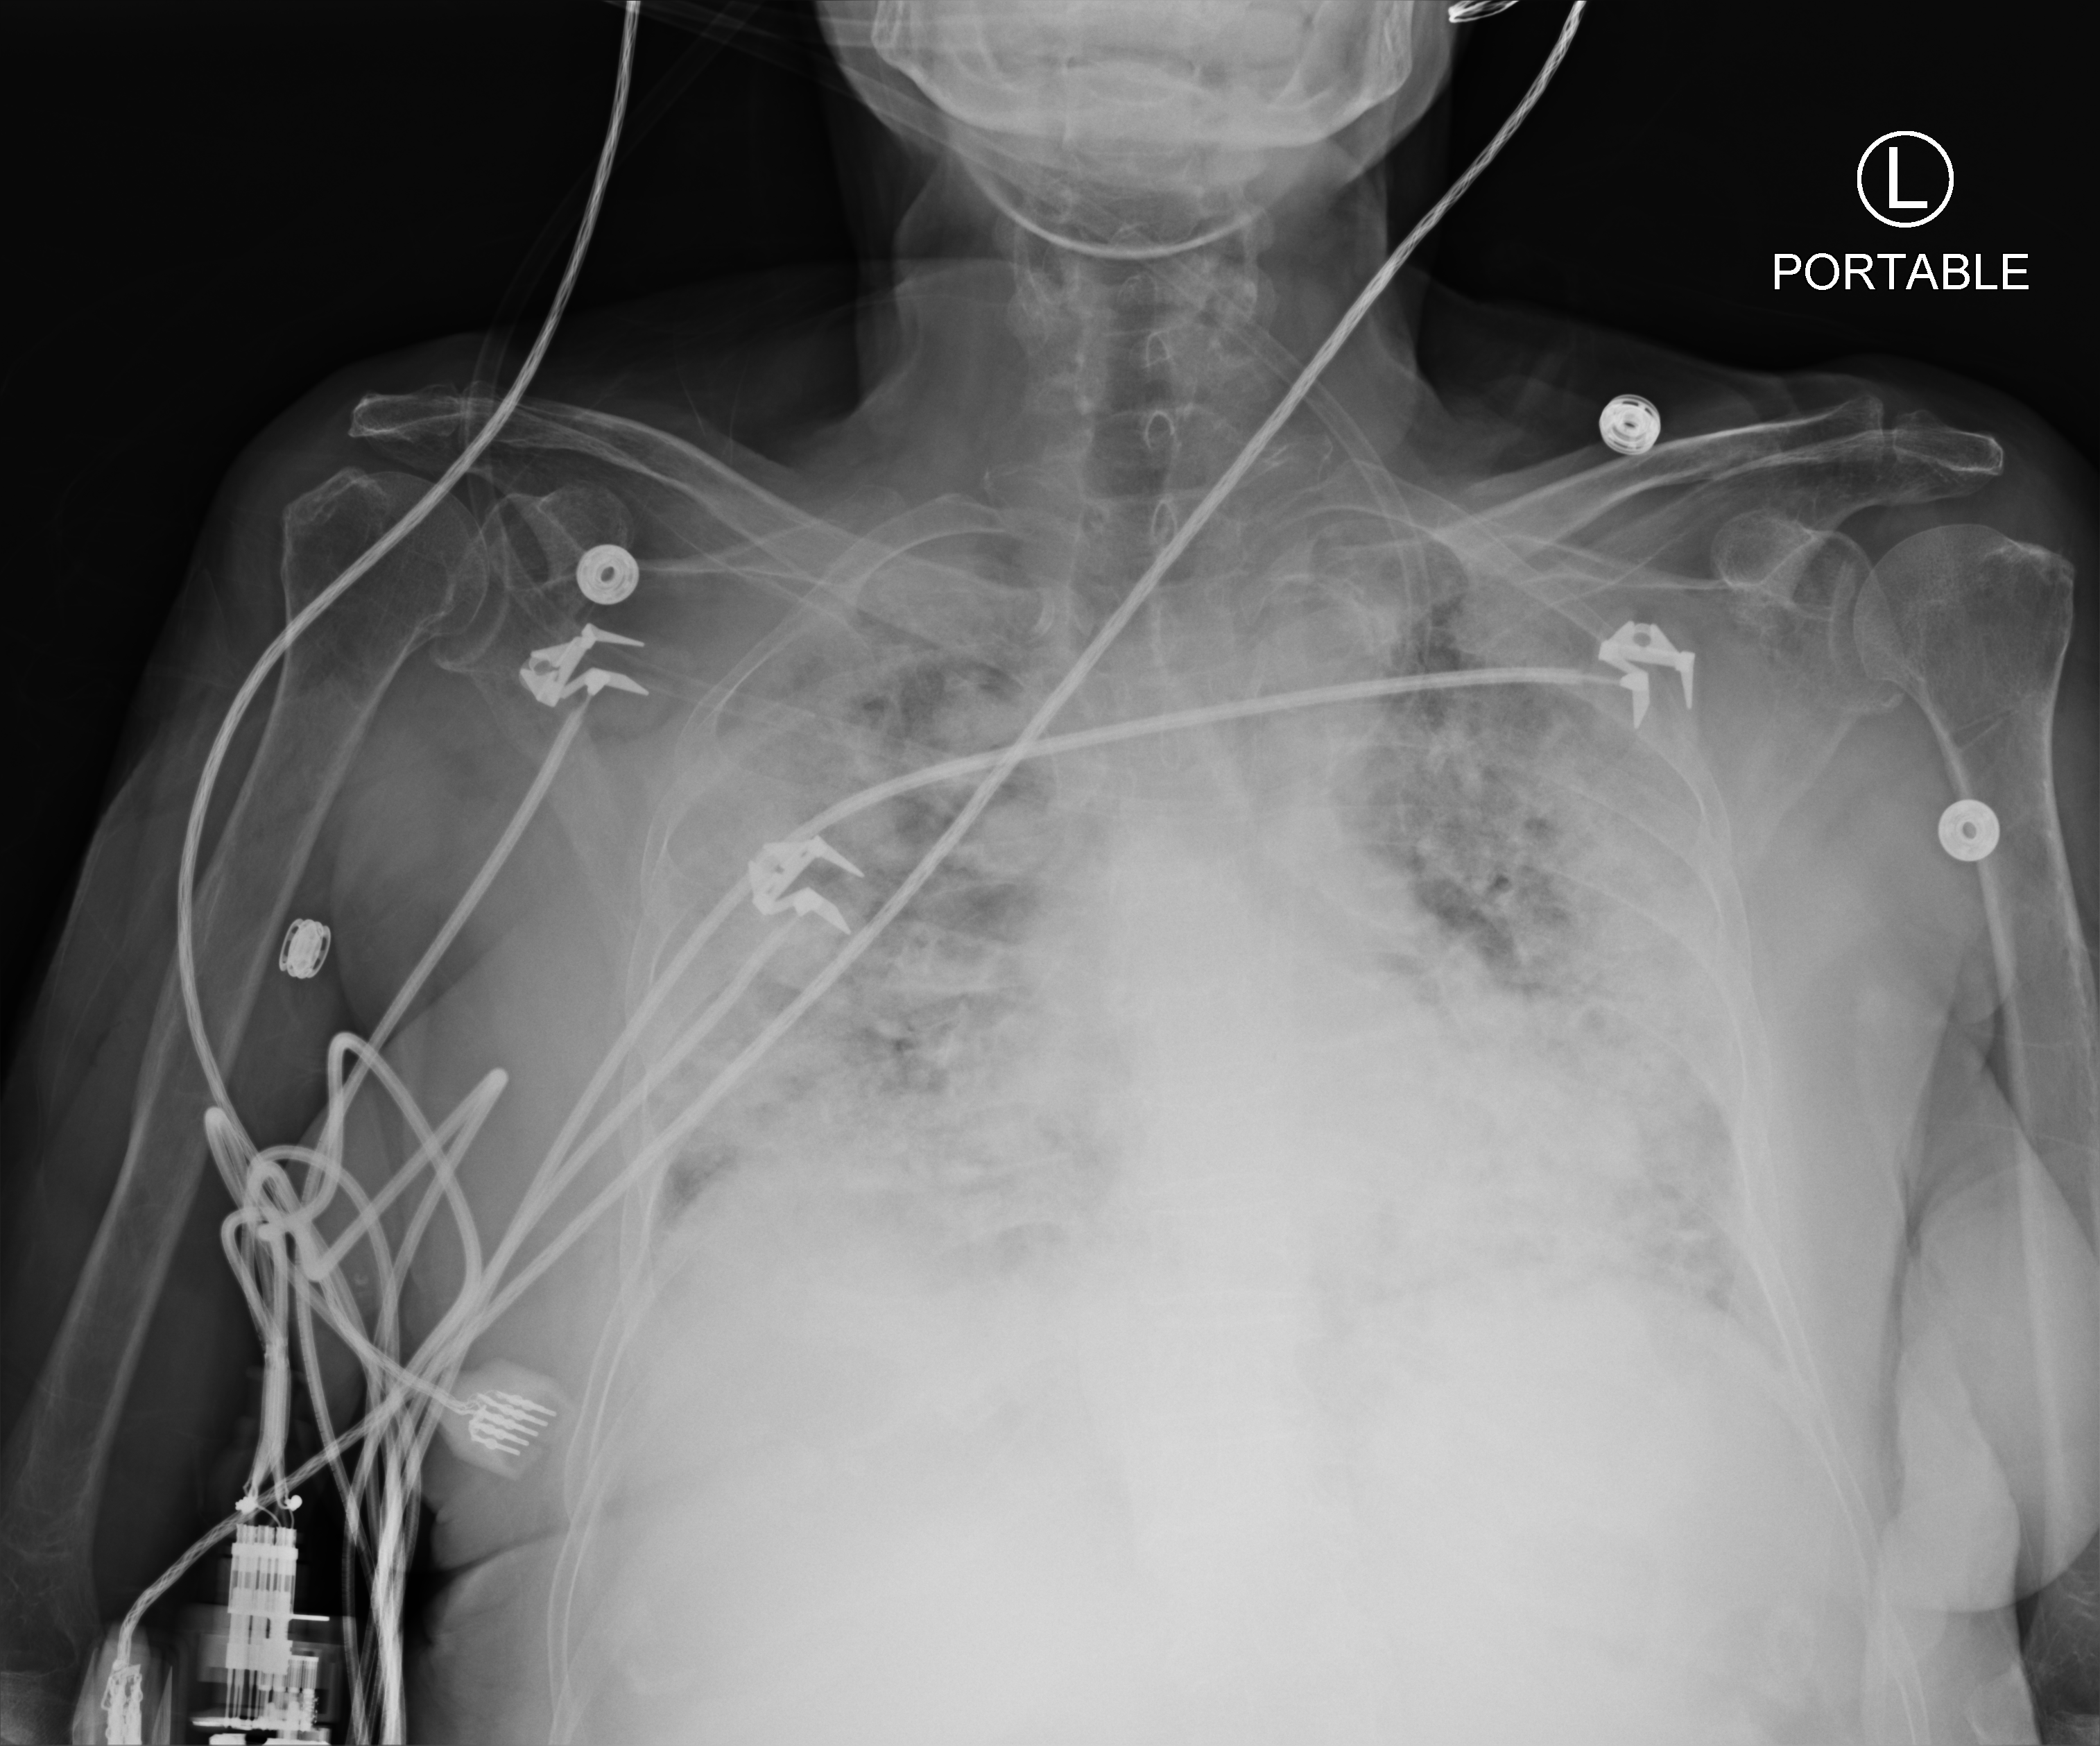
Chest X-ray (portable); anteroposterior (AP) projection. Female patient hospitalised with COVID-19, age 75–90 years.
Admission-level facts for this patient (not findings on this image; timing relative to this image not recorded): diabetes (admission record): yes; mechanically ventilated during this hospital stay: no.